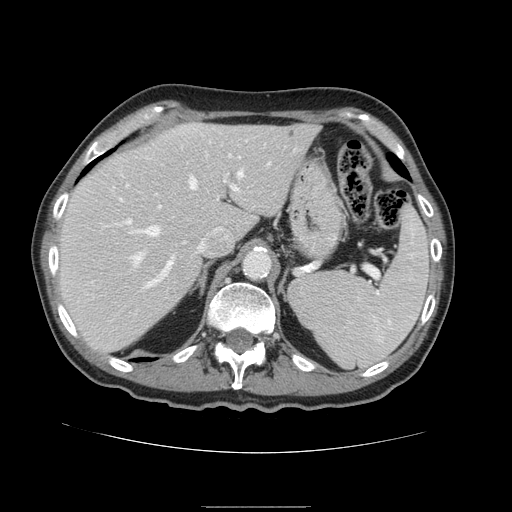
Contrast-enhanced abdominal CT, one axial slice; position 109 of 168 along the scan axis; soft-tissue window (W 400 / L 40 HU); 2.5 mm slice thickness; 512 × 512 image matrix, field of view 386 × 386 mm. Male patient, age 74 years. Case-level facts recorded for this patient, not image findings: diagnosis: colorectal cancer liver metastases, imaged before liver resection; multiple liver metastases: no; largest metastasis: 14.5 cm; disease in both lobes: yes.
Structures marked on this image (expert manual segmentation):
- hepatic veins: bounding box [x1, y1, x2, y2] px = [136, 171, 243, 263]
- liver: [59, 123, 320, 352]
- planned liver remnant (the part of the liver to remain after resection): [59, 124, 321, 352]
- portal vein (with intrahepatic branches): [93, 187, 238, 289]